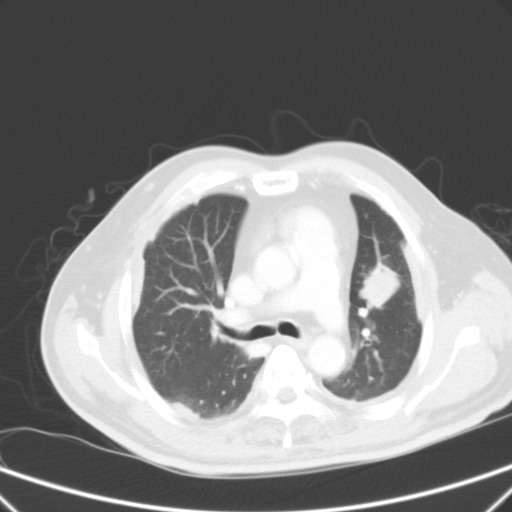
Chest CT, one axial slice; slice 39 of 59 in the series (ordered by position); 120 kVp; intravenous contrast given; lung window (W 1500 / L -600 HU); 512 × 512 image matrix, field of view 357 × 357 mm. Patient: male, 66 years. Case-level facts recorded for this patient, not image findings: clinical TNM (as recorded): T1c N3 M1a.
Annotated regions visible in this slice (bounding box drawn by a radiologist):
- lung tumour (recorded histology: squamous cell carcinoma): bounding box (x1, y1, x2, y2) in pixels: (355, 261, 408, 323)